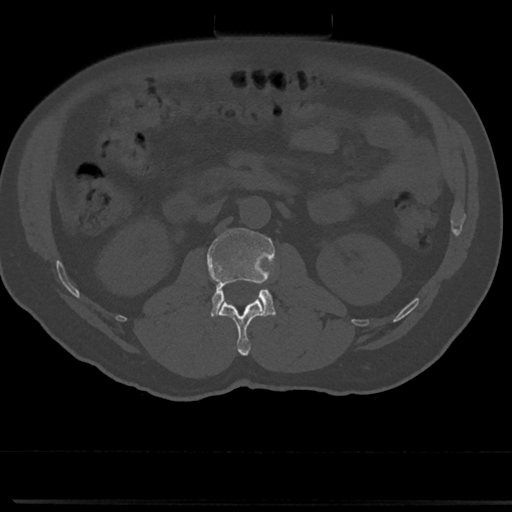
CT including the spine, one axial slice. Slice 42 of 817 in the series (ordered by position). 120 kVp. Bone window (W 1800 / L 400 HU). 0.5 mm slice thickness. 512 × 512 image matrix, field of view 355 × 355 mm. Patient: male, 61 years. From the clinical record (not read from this slice): primary cancer: prostate.
Annotated regions visible in this slice (semi-automatic segmentation, software-assisted and operator-edited):
- L1 vertebra: bounding box [x1, y1, x2, y2] px = [219, 299, 264, 355]
- L2 vertebra: [207, 228, 274, 317]